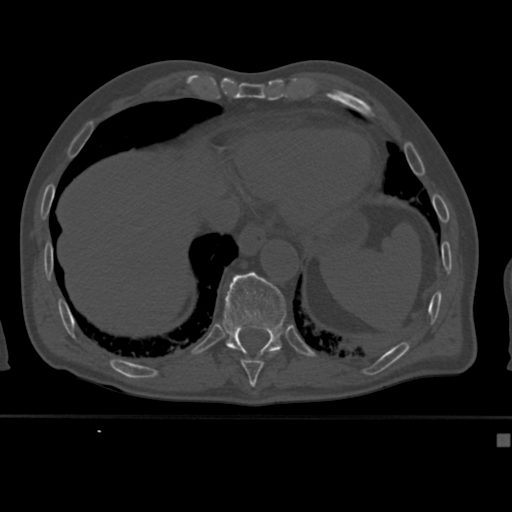
CT including the spine, one axial slice; position 219 of 430 along the scan axis; reconstruction kernel Br40s; bone window (W 1800 / L 400 HU); 512 × 512 image matrix, field of view 337 × 337 mm. Male patient, age 64 years. From the clinical record (not read from this slice): primary cancer: uterus; vertebrae with lytic lesions (as recorded): T1, T4, T5, T7, L5.
Annotated regions visible in this slice (semi-automatically segmented with operator editing):
- T10 vertebra: bounding box [x1, y1, x2, y2] px = [241, 356, 264, 382]
- T11 vertebra: [222, 271, 287, 356]